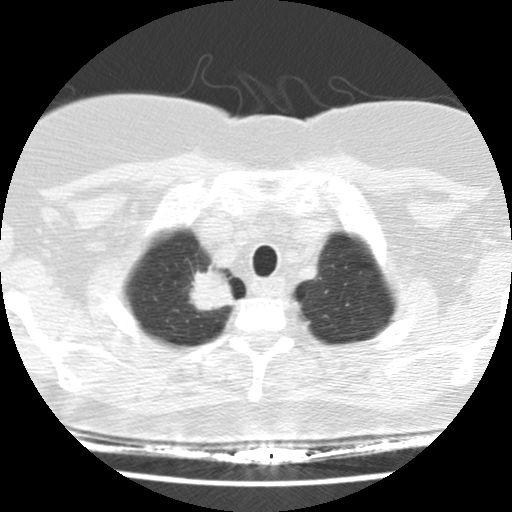
Low-dose screening chest CT, one axial slice. Position 133 of 148 along the scan axis. Reconstruction kernel STANDARD. 120 kVp. Lung window (W 1500 / L -600 HU). 2.5 mm slice thickness. 512 × 512 image matrix, field of view 281 × 281 mm.
Outlined on this slice (expert manual segmentation):
- lesion 1 (tumor, upper lobe of right lung): bounding box <190,270,234,311> (left, top, right, bottom; pixels)